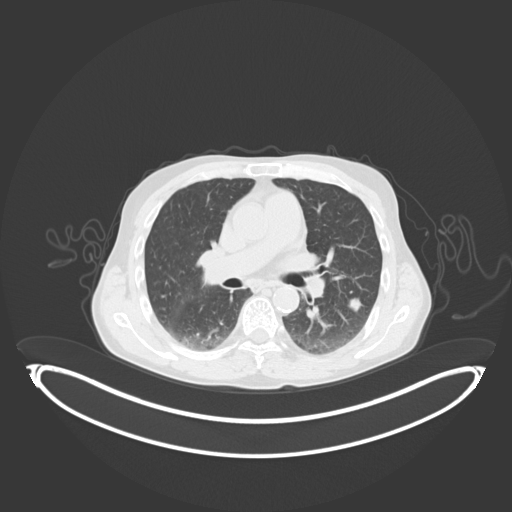
Chest CT, one axial slice. Position 55 of 102 along the scan axis. Lung window (W 1500 / L -600 HU). 3 mm slice thickness. 512 × 512 image matrix, field of view 500 × 500 mm. Patient: male, 58 years. Case-level facts recorded for this patient, not image findings: clinical TNM (as recorded): T1c N0 M0; histopathological grade: G2.
Structures marked on this image (rectangle marked by the reading radiologist):
- lung tumour (recorded histology: adenocarcinoma): box from (x=348, y=295) to (x=365, y=314) px